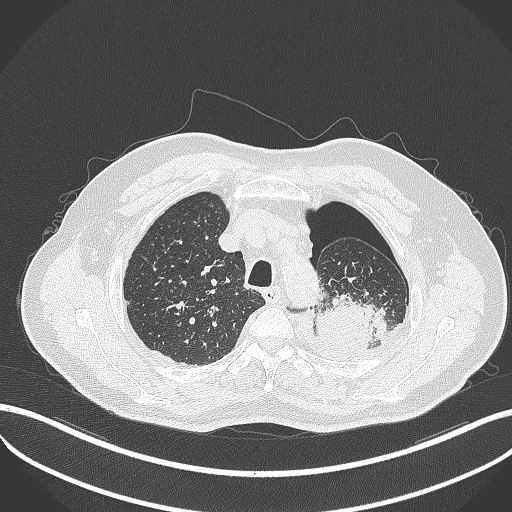
Chest CT, one axial slice. Slice 404 of 464 in the series (ordered by position). Reconstruction kernel B70f. 120 kVp. Lung window (W 1500 / L -600 HU). 512 × 512 image matrix. Patient: male, 76 years. Case-level facts recorded for this patient, not image findings: clinical TNM (as recorded): T3 N0 M1b.
Annotated regions visible in this slice (rectangle marked by the reading radiologist):
- lung tumour (recorded histology: adenocarcinoma): box from (x=314, y=288) to (x=386, y=352) px